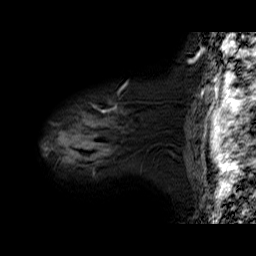
Breast MRI (dynamic contrast-enhanced), one sagittal slice; position 55 of 60 along the scan axis; dynamic contrast-enhanced series, time point 2 of 6 at this slice position (early post-contrast); 1.5 T; TE 6.3 ms, TR 32.9 ms; 4 mm slice thickness; 256 × 256 image matrix, field of view 200 × 200 mm. Female patient. Case-level facts recorded for this patient, not image findings: setting: breast cancer imaged before/during neoadjuvant chemotherapy; receptor status: HER2-positive.
Outlined on this slice (semi-automatically segmented with operator editing):
- analysis volume of interest (the breast-tissue region the enhancement analysis was run in; not a lesion): bounding box (x1, y1, x2, y2) in pixels: (46, 85, 176, 171)
- tumour enhancement mask (voxels above the 100 % enhancement threshold inside the analysis volume of interest): (115, 108, 117, 111)